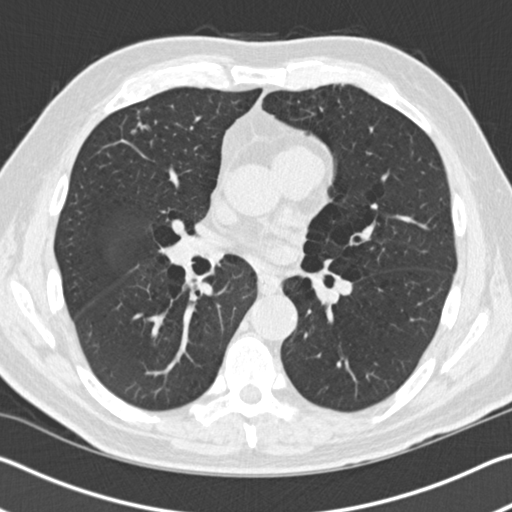
Axial slice from a low-dose chest CT screening exam. First (baseline) screen. Lung window (W 1500 / L -600 HU). 2 mm slice thickness. Standard (soft-tissue) reconstruction kernel (B30f). Slice 85 of 165 in the series. 512 × 512 image matrix, field of view 340 × 340 mm. Male, age 69 years at enrolment.
Expert reader's lesion annotation, box from (x=119, y=95) to (x=171, y=145) px. No non-calcified nodule or mass ≥4 mm was recorded by the screening reader at this exam. Official screen result: negative screen, significant abnormalities not suspicious for lung cancer.